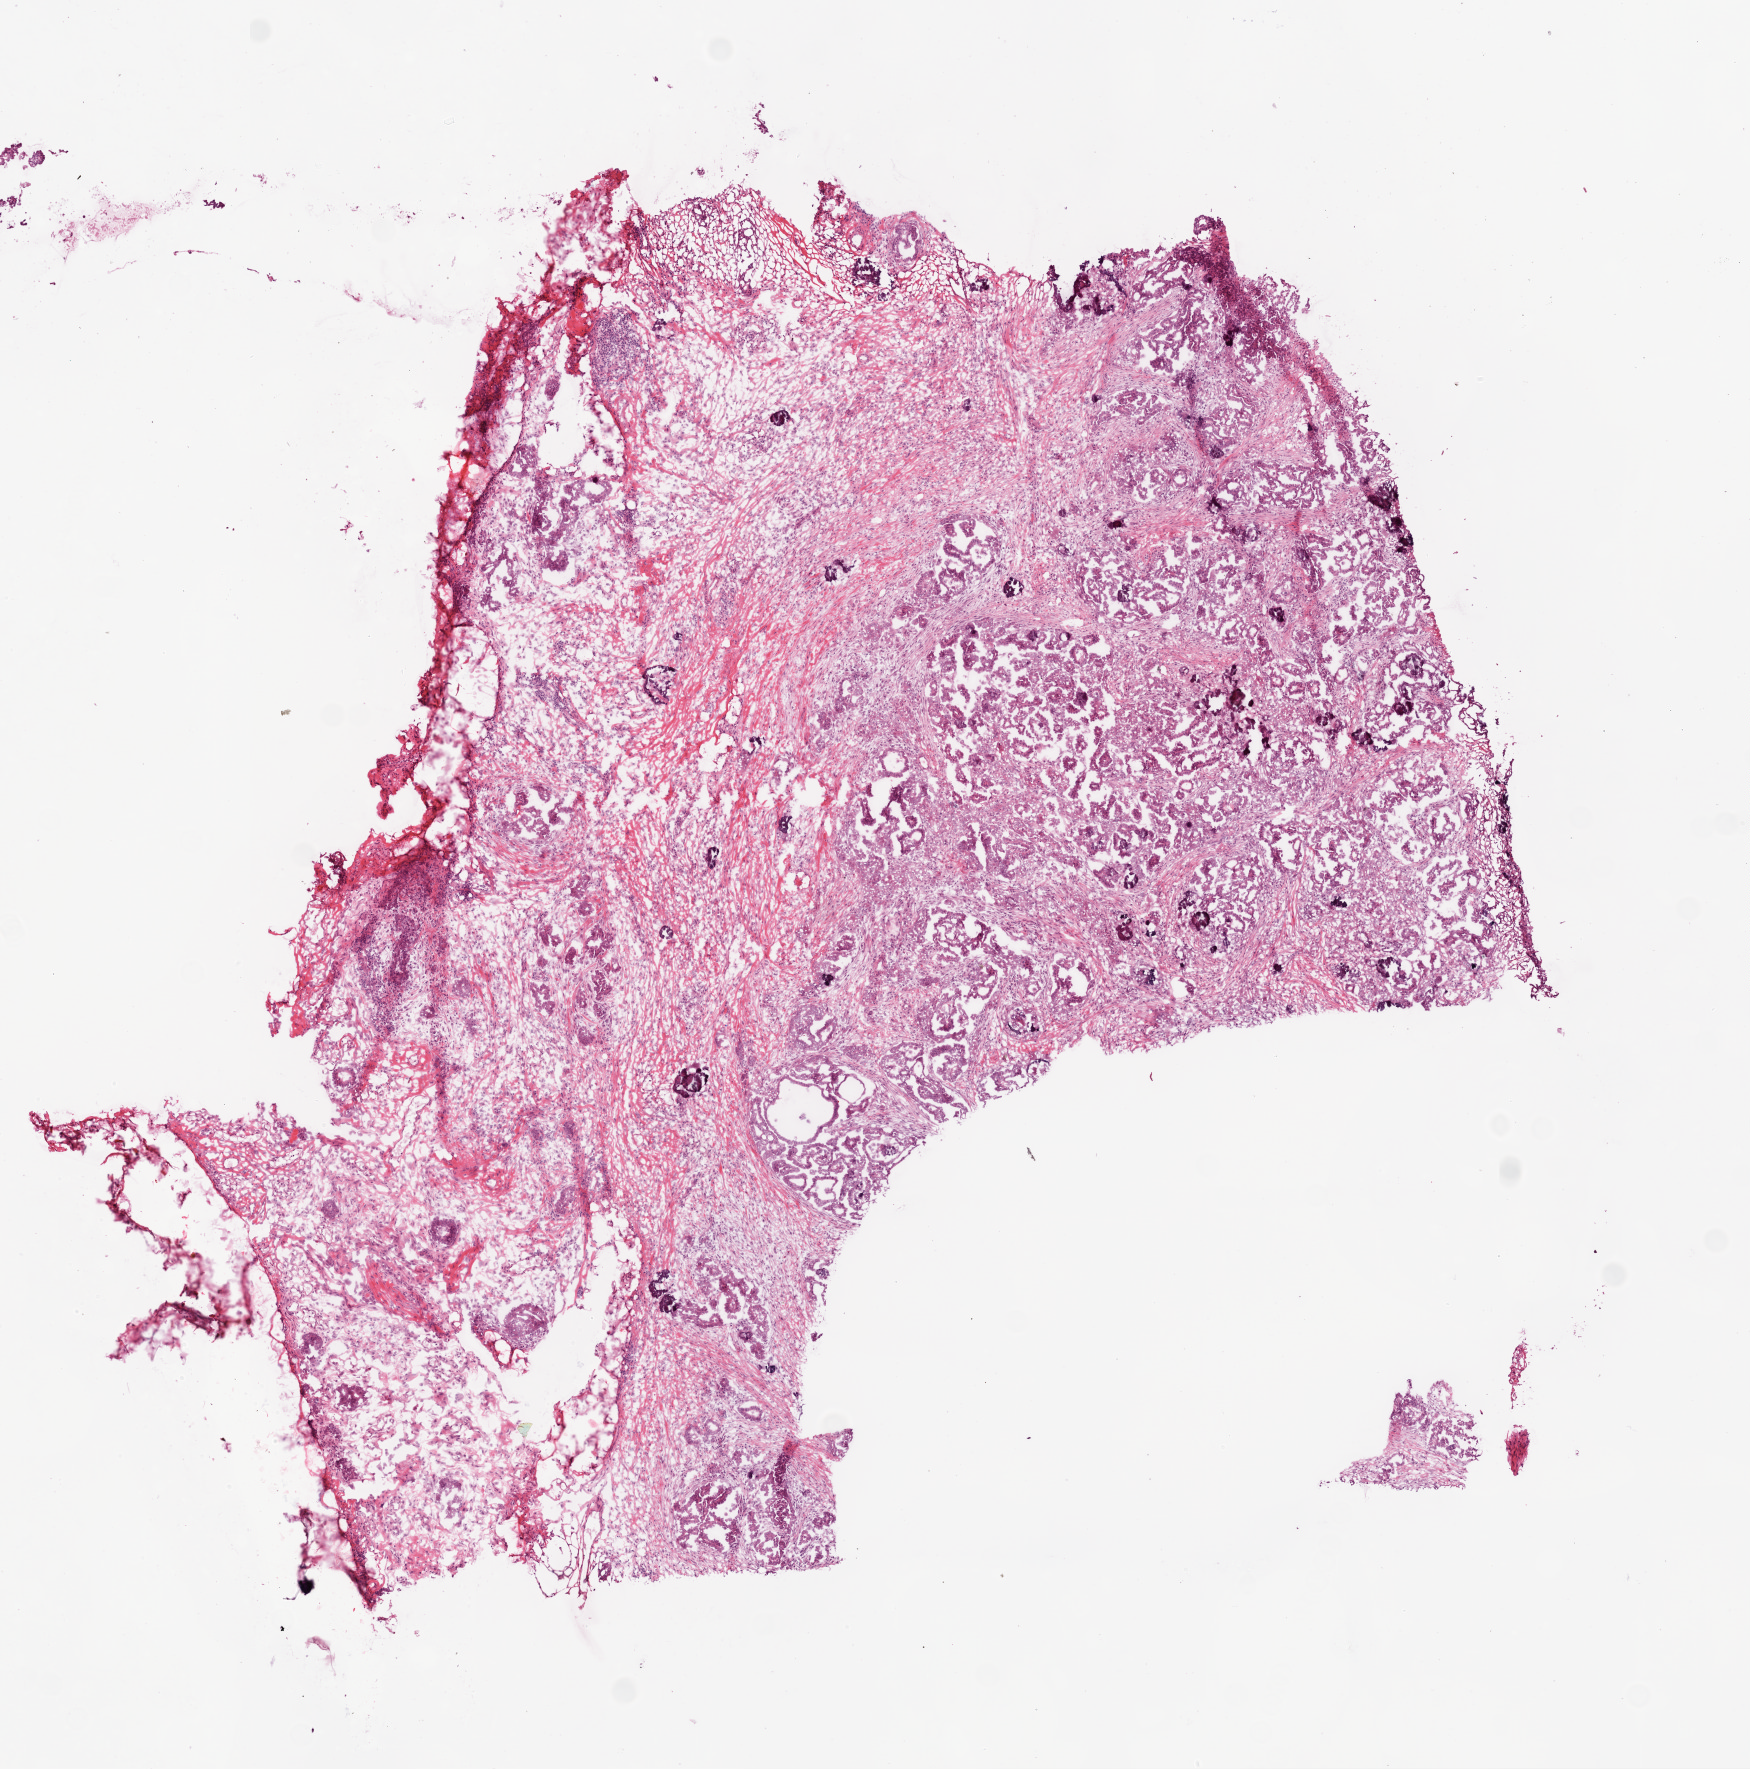
Whole-slide histology image, H&E-stained, a low-resolution overview of the entire scanned area, about 7.0 x 7.1 mm; frozen section; sample: recurrent tumour, ovary. Female, age 54 years at initial diagnosis. Slide review estimates, as recorded: tumour cells 75%, tumour nuclei 75%.
This section: recurrent tumour. Patient diagnosis: Serous cystadenocarcinoma, NOS.